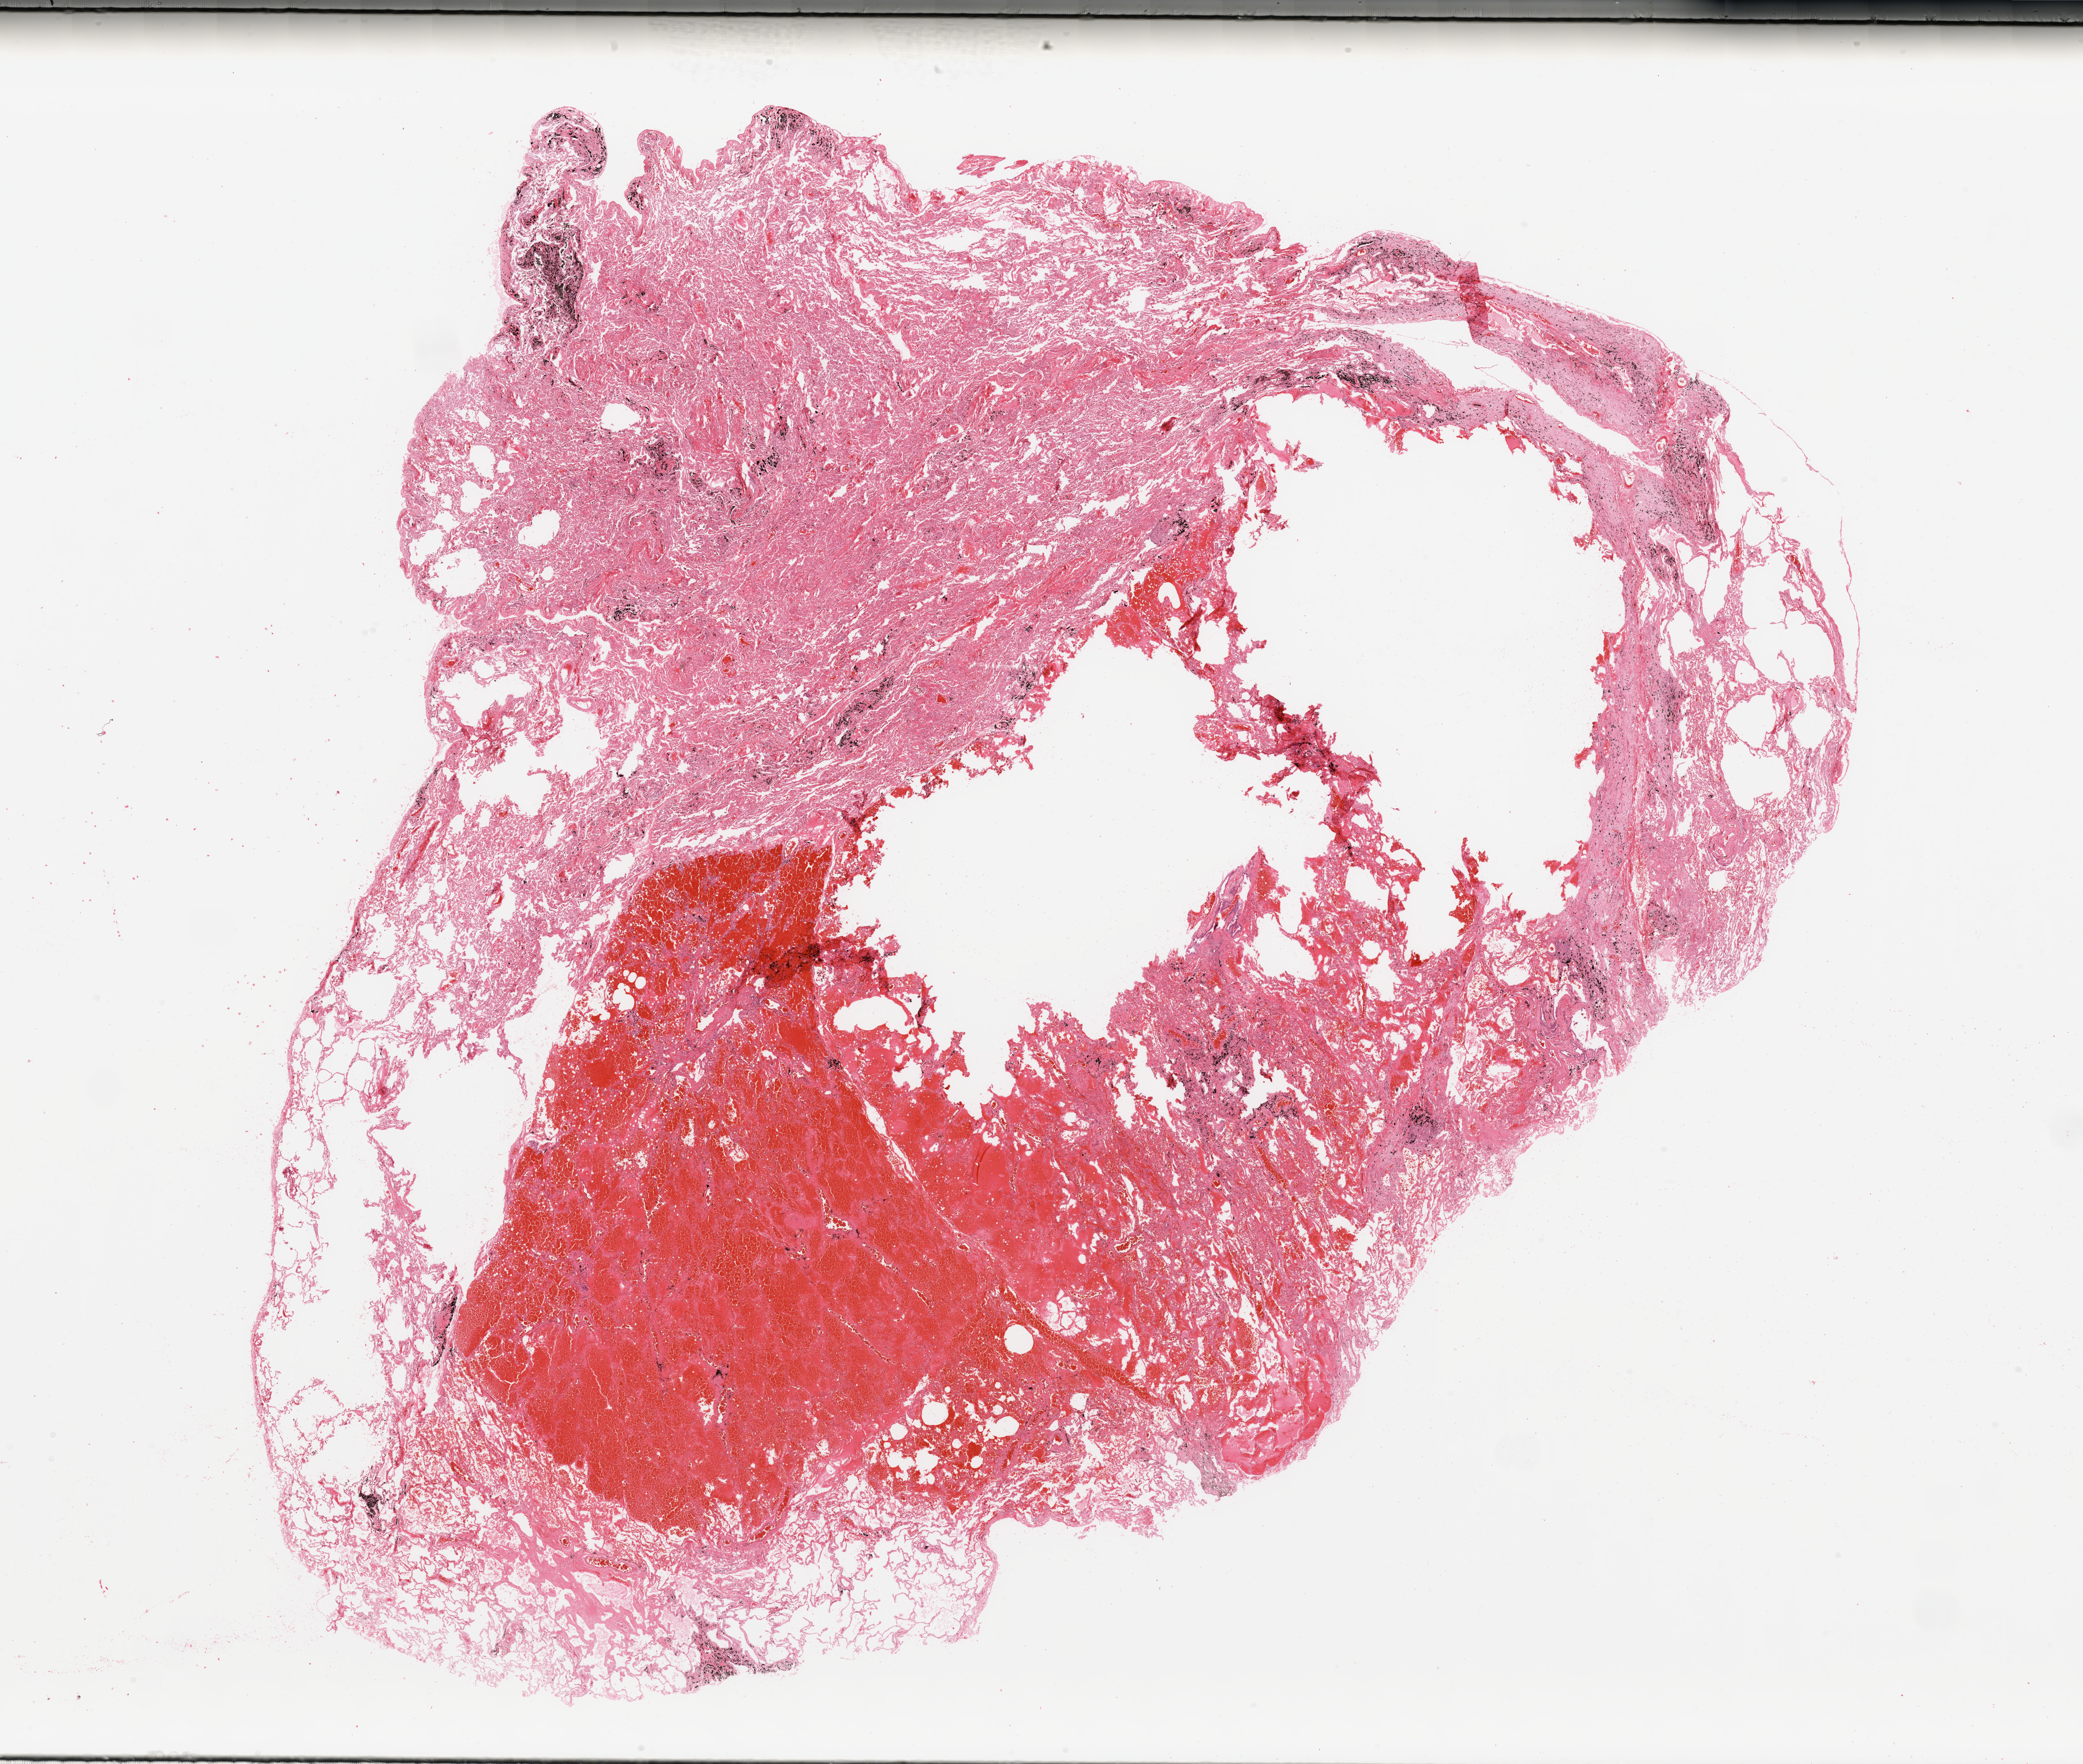
Digitized H&E tissue section (whole slide), shown as a low-resolution overview of the whole scanned area (about 28.5 x 24.2 mm, from a 20x scan), normal (non-tumour) tissue sample, sampled site: lung. Patient: male, age 63 years.
• this section: normal (non-tumour) tissue from the same patient
• patient diagnosis: Adenocarcinoma, NOS